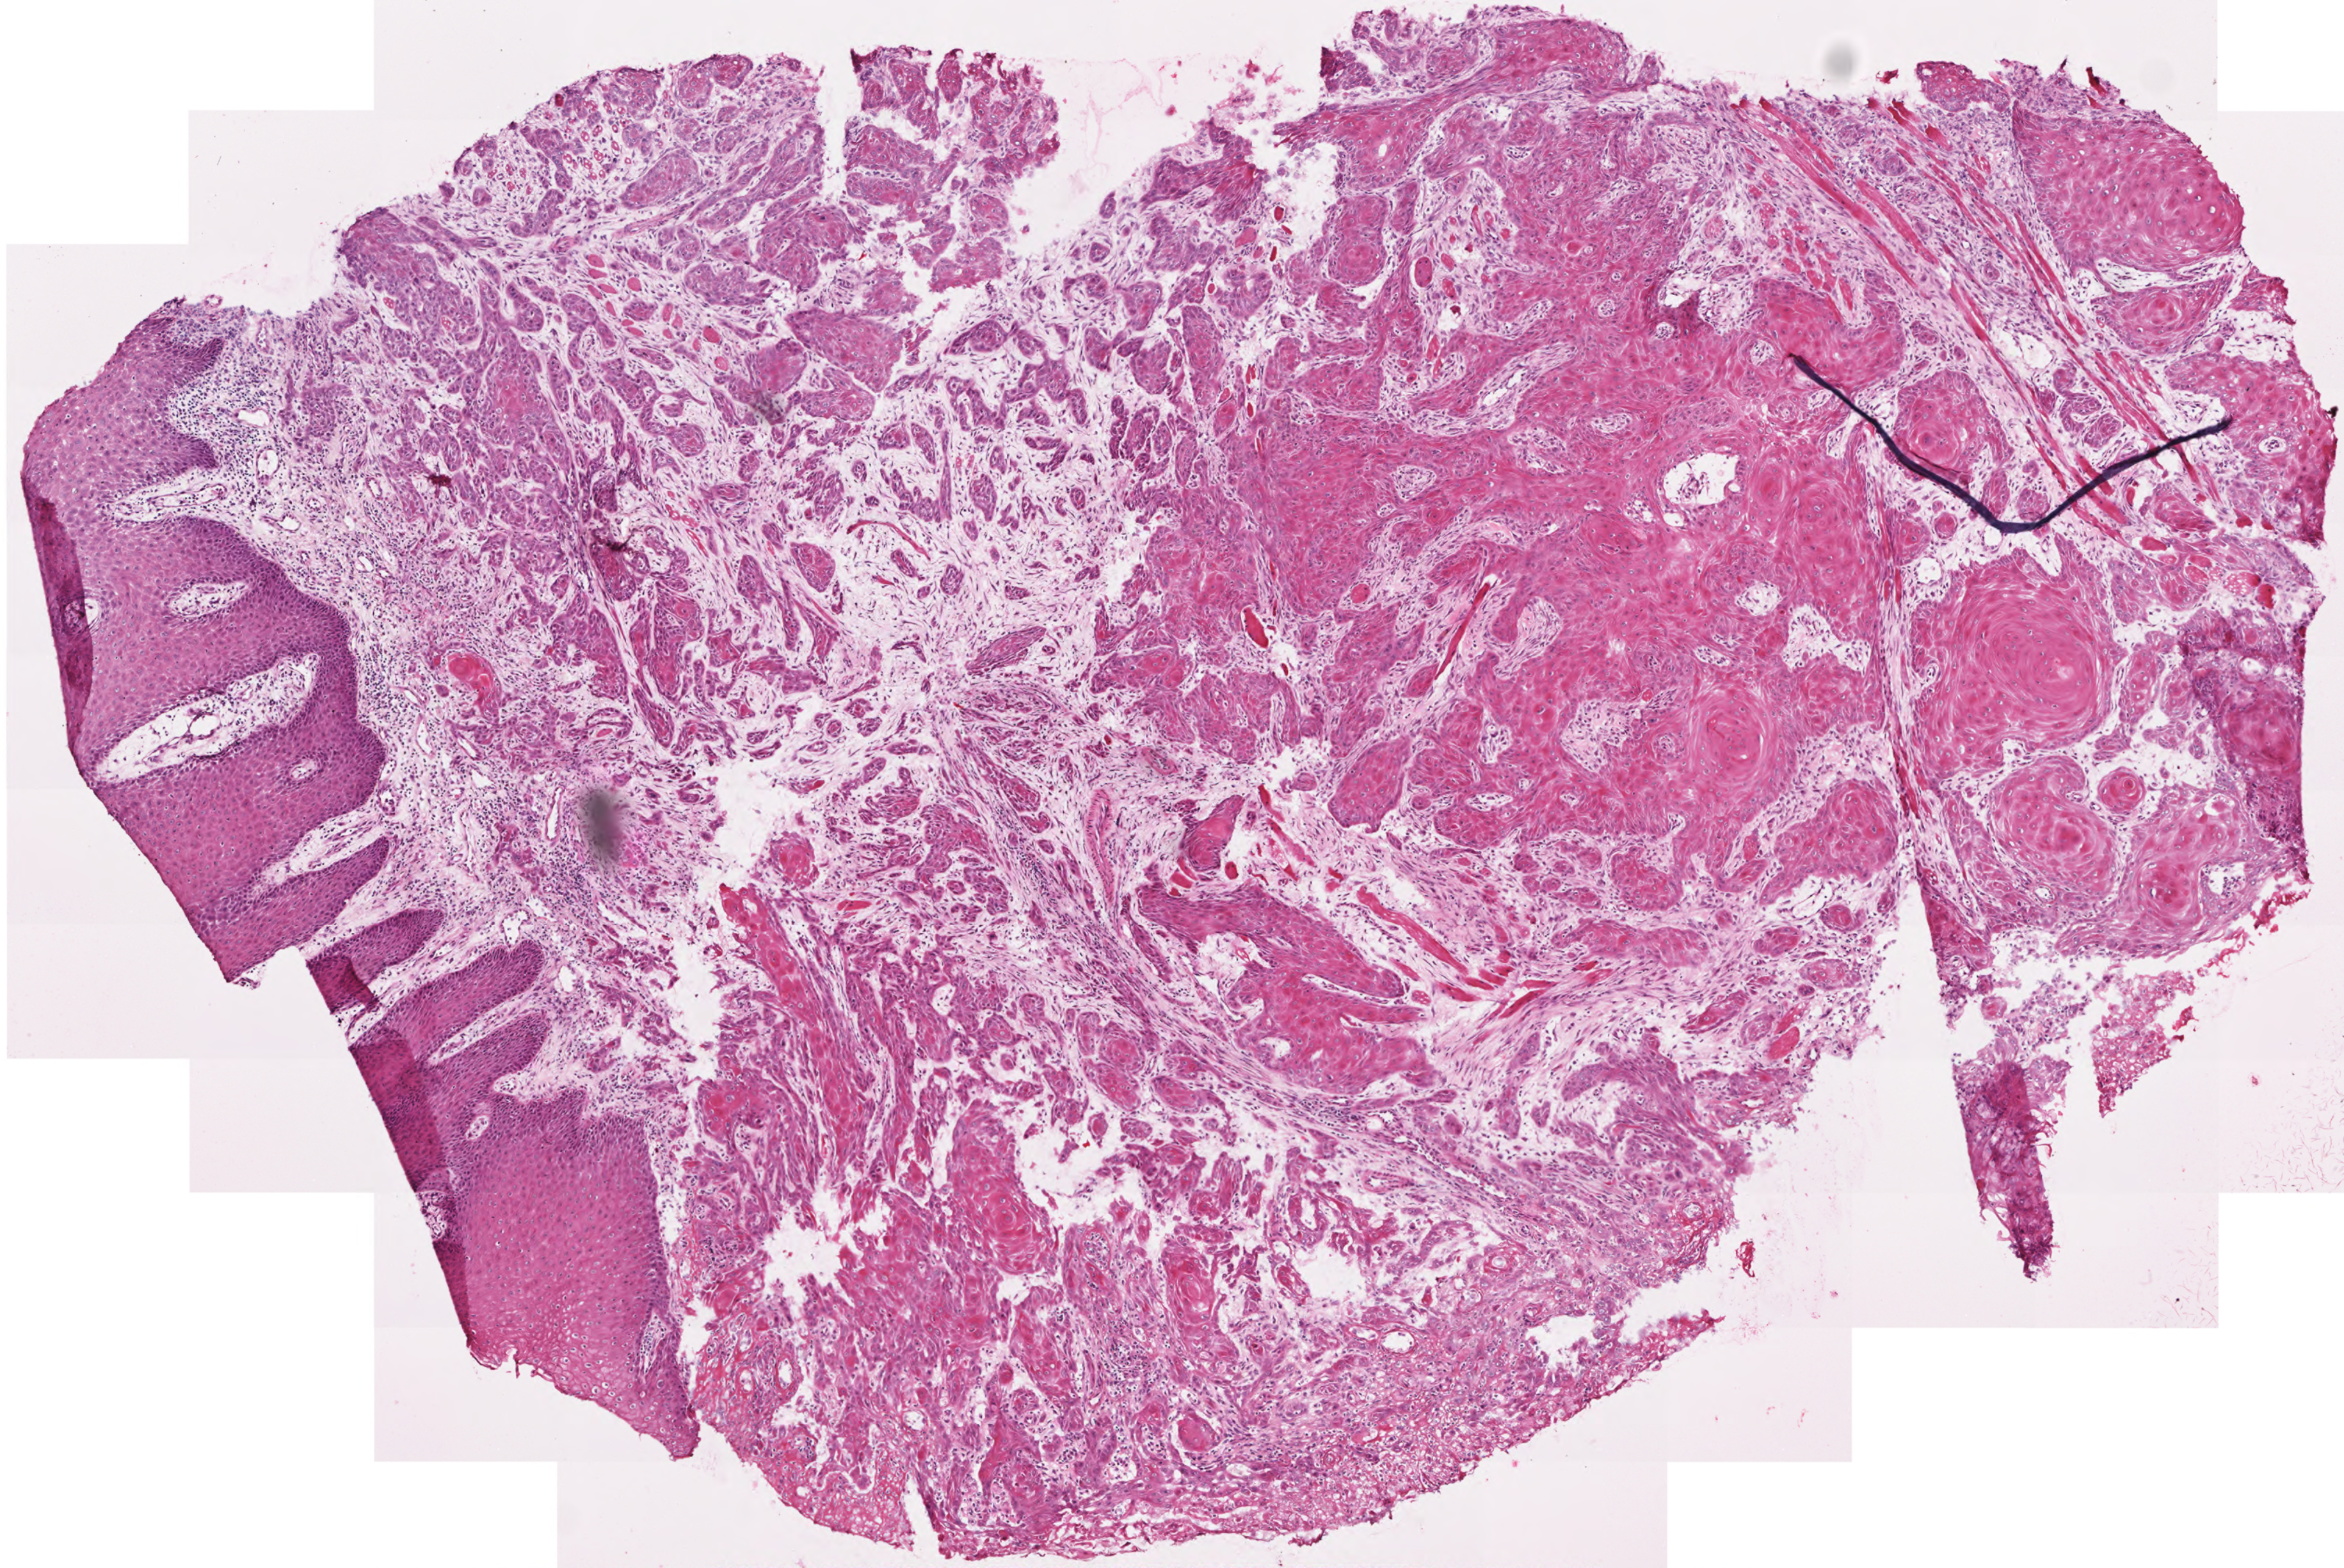
H&E-stained whole-slide image, shown as a low-resolution overview of the whole scanned area (about 3.4 x 2.3 mm); frozen section from the top of the tissue portion; primary tumour sample from the head and neck. Patient: male, age at initial diagnosis 64 years. Histologic grade: G2 (moderately differentiated). Pathologist review of this section (percent, as recorded): tumour cells 78%, tumour nuclei 75%, normal cells 12%, stromal cells 10%, necrosis 0%. Infiltration values recorded for this section: lymphocyte infiltration 10%.
* AJCC pathologic stage: I (6th edition)
* histologic diagnosis: Squamous cell carcinoma, NOS (tongue, NOS)
* laterality: right
* TNM: T1 N0 M0